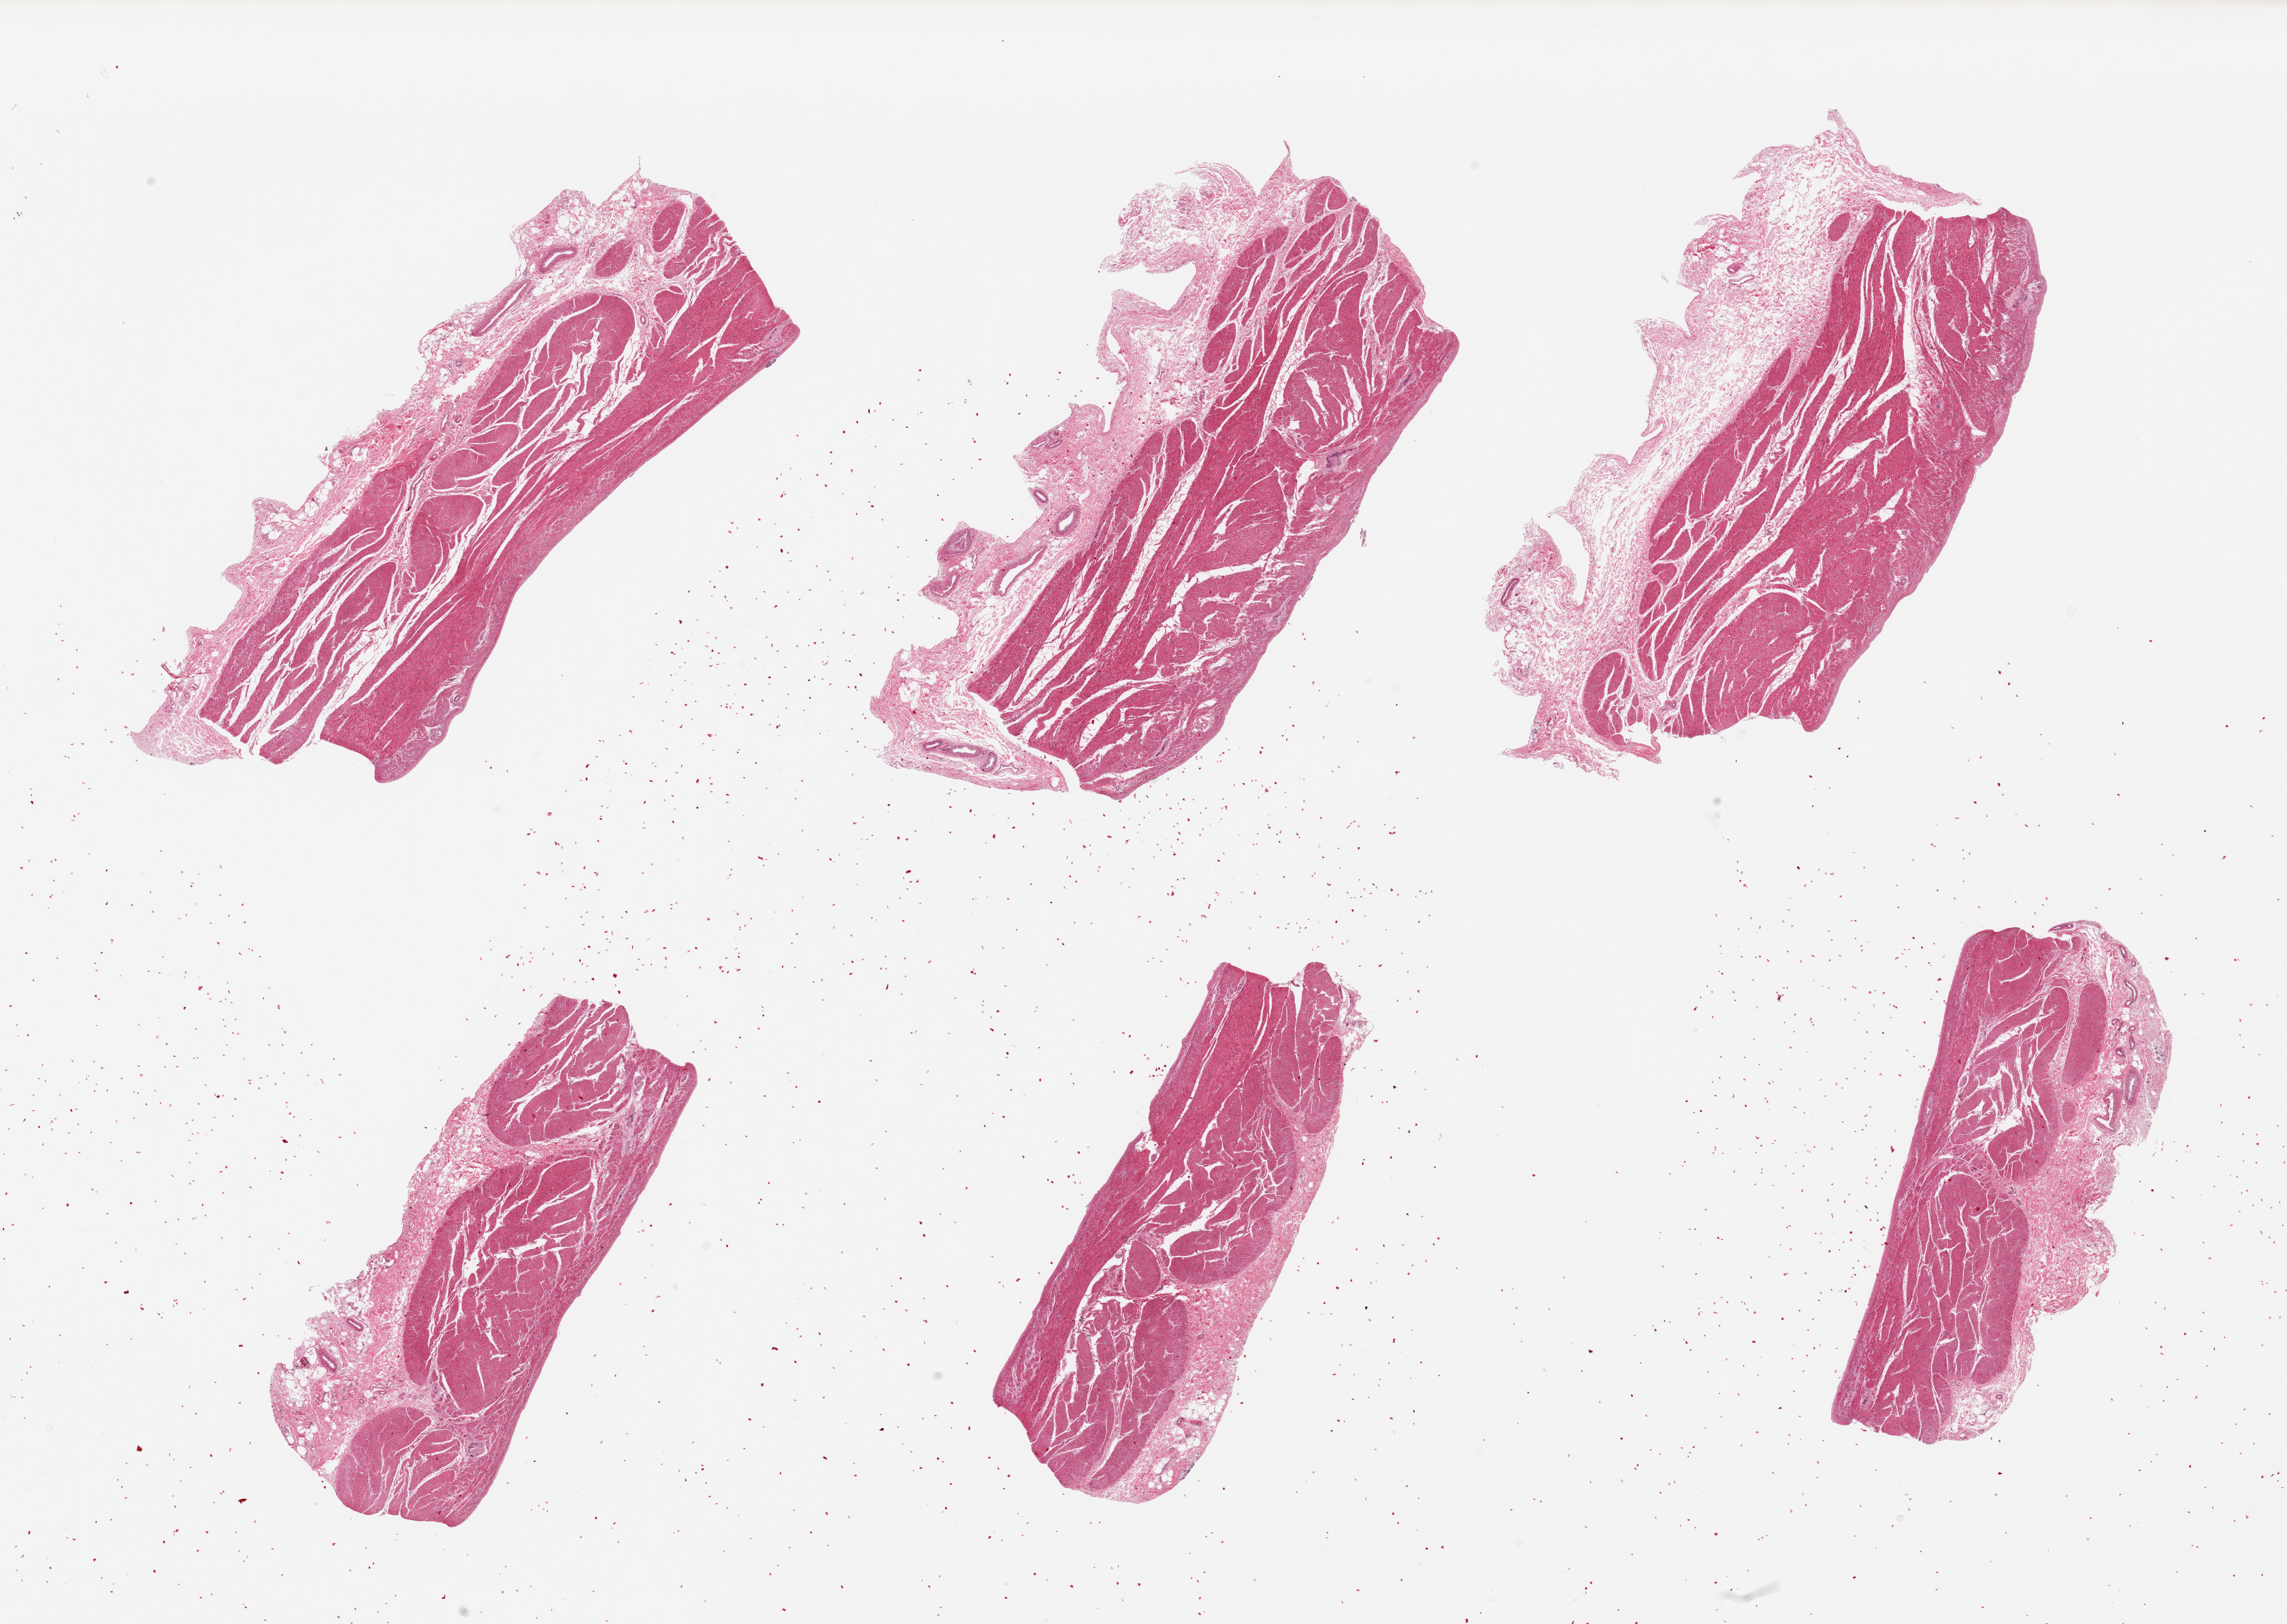
Digitized hematoxylin and eosin (H&E)-stained section, brightfield, shown as a low-resolution overview of the whole scanned area (about 26.6 x 18.9 mm); PAXgene-fixed, paraffin-embedded tissue; section of stomach (target tissue); donor tissue sample. Donor sex: male.
Pathologist's review note for this sample: 6 pieces; muscularis and submucosa only (full thickness sections preferred with trimming of muscularis as necessary).